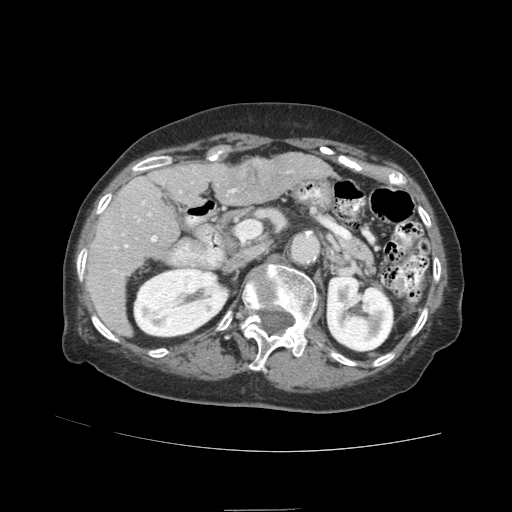
Contrast-enhanced abdominal CT (liver protocol), one axial slice. Position 46 of 89 along the scan axis. Reconstruction kernel STANDARD. 140 kVp. Soft-tissue window (W 400 / L 40 HU). 2.5 mm slice thickness. 512 × 512 image matrix, field of view 360 × 360 mm. From the clinical record (not read from this slice): diagnosis: hepatocellular carcinoma (patient treated with transarterial chemoembolisation; whether this scan precedes or follows treatment is not stated here); TNM stage (as recorded): Stage-II; Child-Pugh class: A; tumour nodularity: multinodular; tumour size: 4 cm.
Structures marked on this image (semi-automatically segmented with operator editing):
- liver parenchyma outside the tumour (the mass and vessels are separate outlines, so this box may not span the whole liver): bounding box (x1, y1, x2, y2) in pixels: (86, 154, 331, 336)
- mass: (234, 158, 272, 202)
- liver vessels: (107, 171, 290, 275)